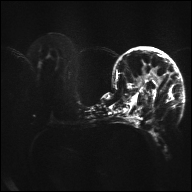
Breast MRI, one axial slice. Position 17 of 32 along the scan axis. Diffusion-weighted series; image 2 of 4 stored at this slice position (different b-values; order by instance number). 1.5 T. 4 mm slice thickness. 192 × 192 image matrix, field of view 360 × 360 mm. Female patient.
Annotated regions visible in this slice (manually delineated by an expert):
- tumour on diffusion-weighted imaging: bounding box <151,67,159,82> (left, top, right, bottom; pixels)